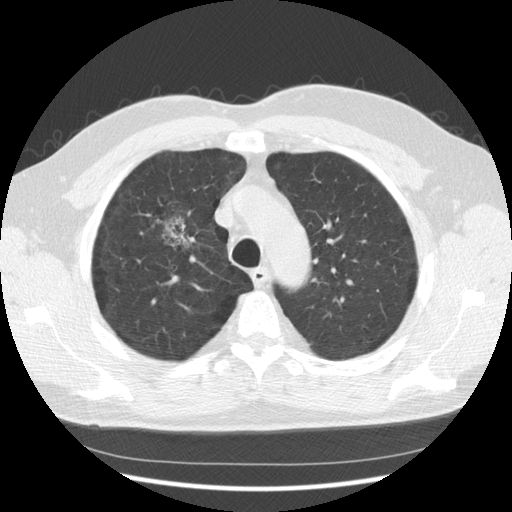
Low-dose screening chest CT, one axial slice. Slice 95 of 133 in the series (ordered by position). Reconstruction kernel STANDARD. Lung window (W 1500 / L -600 HU). 2.5 mm slice thickness. 512 × 512 image matrix.
Structures marked on this image (outlined manually by an expert reader):
- lesion 1 (tumor, upper lobe of right lung): bounding box <162,217,188,247> (left, top, right, bottom; pixels)